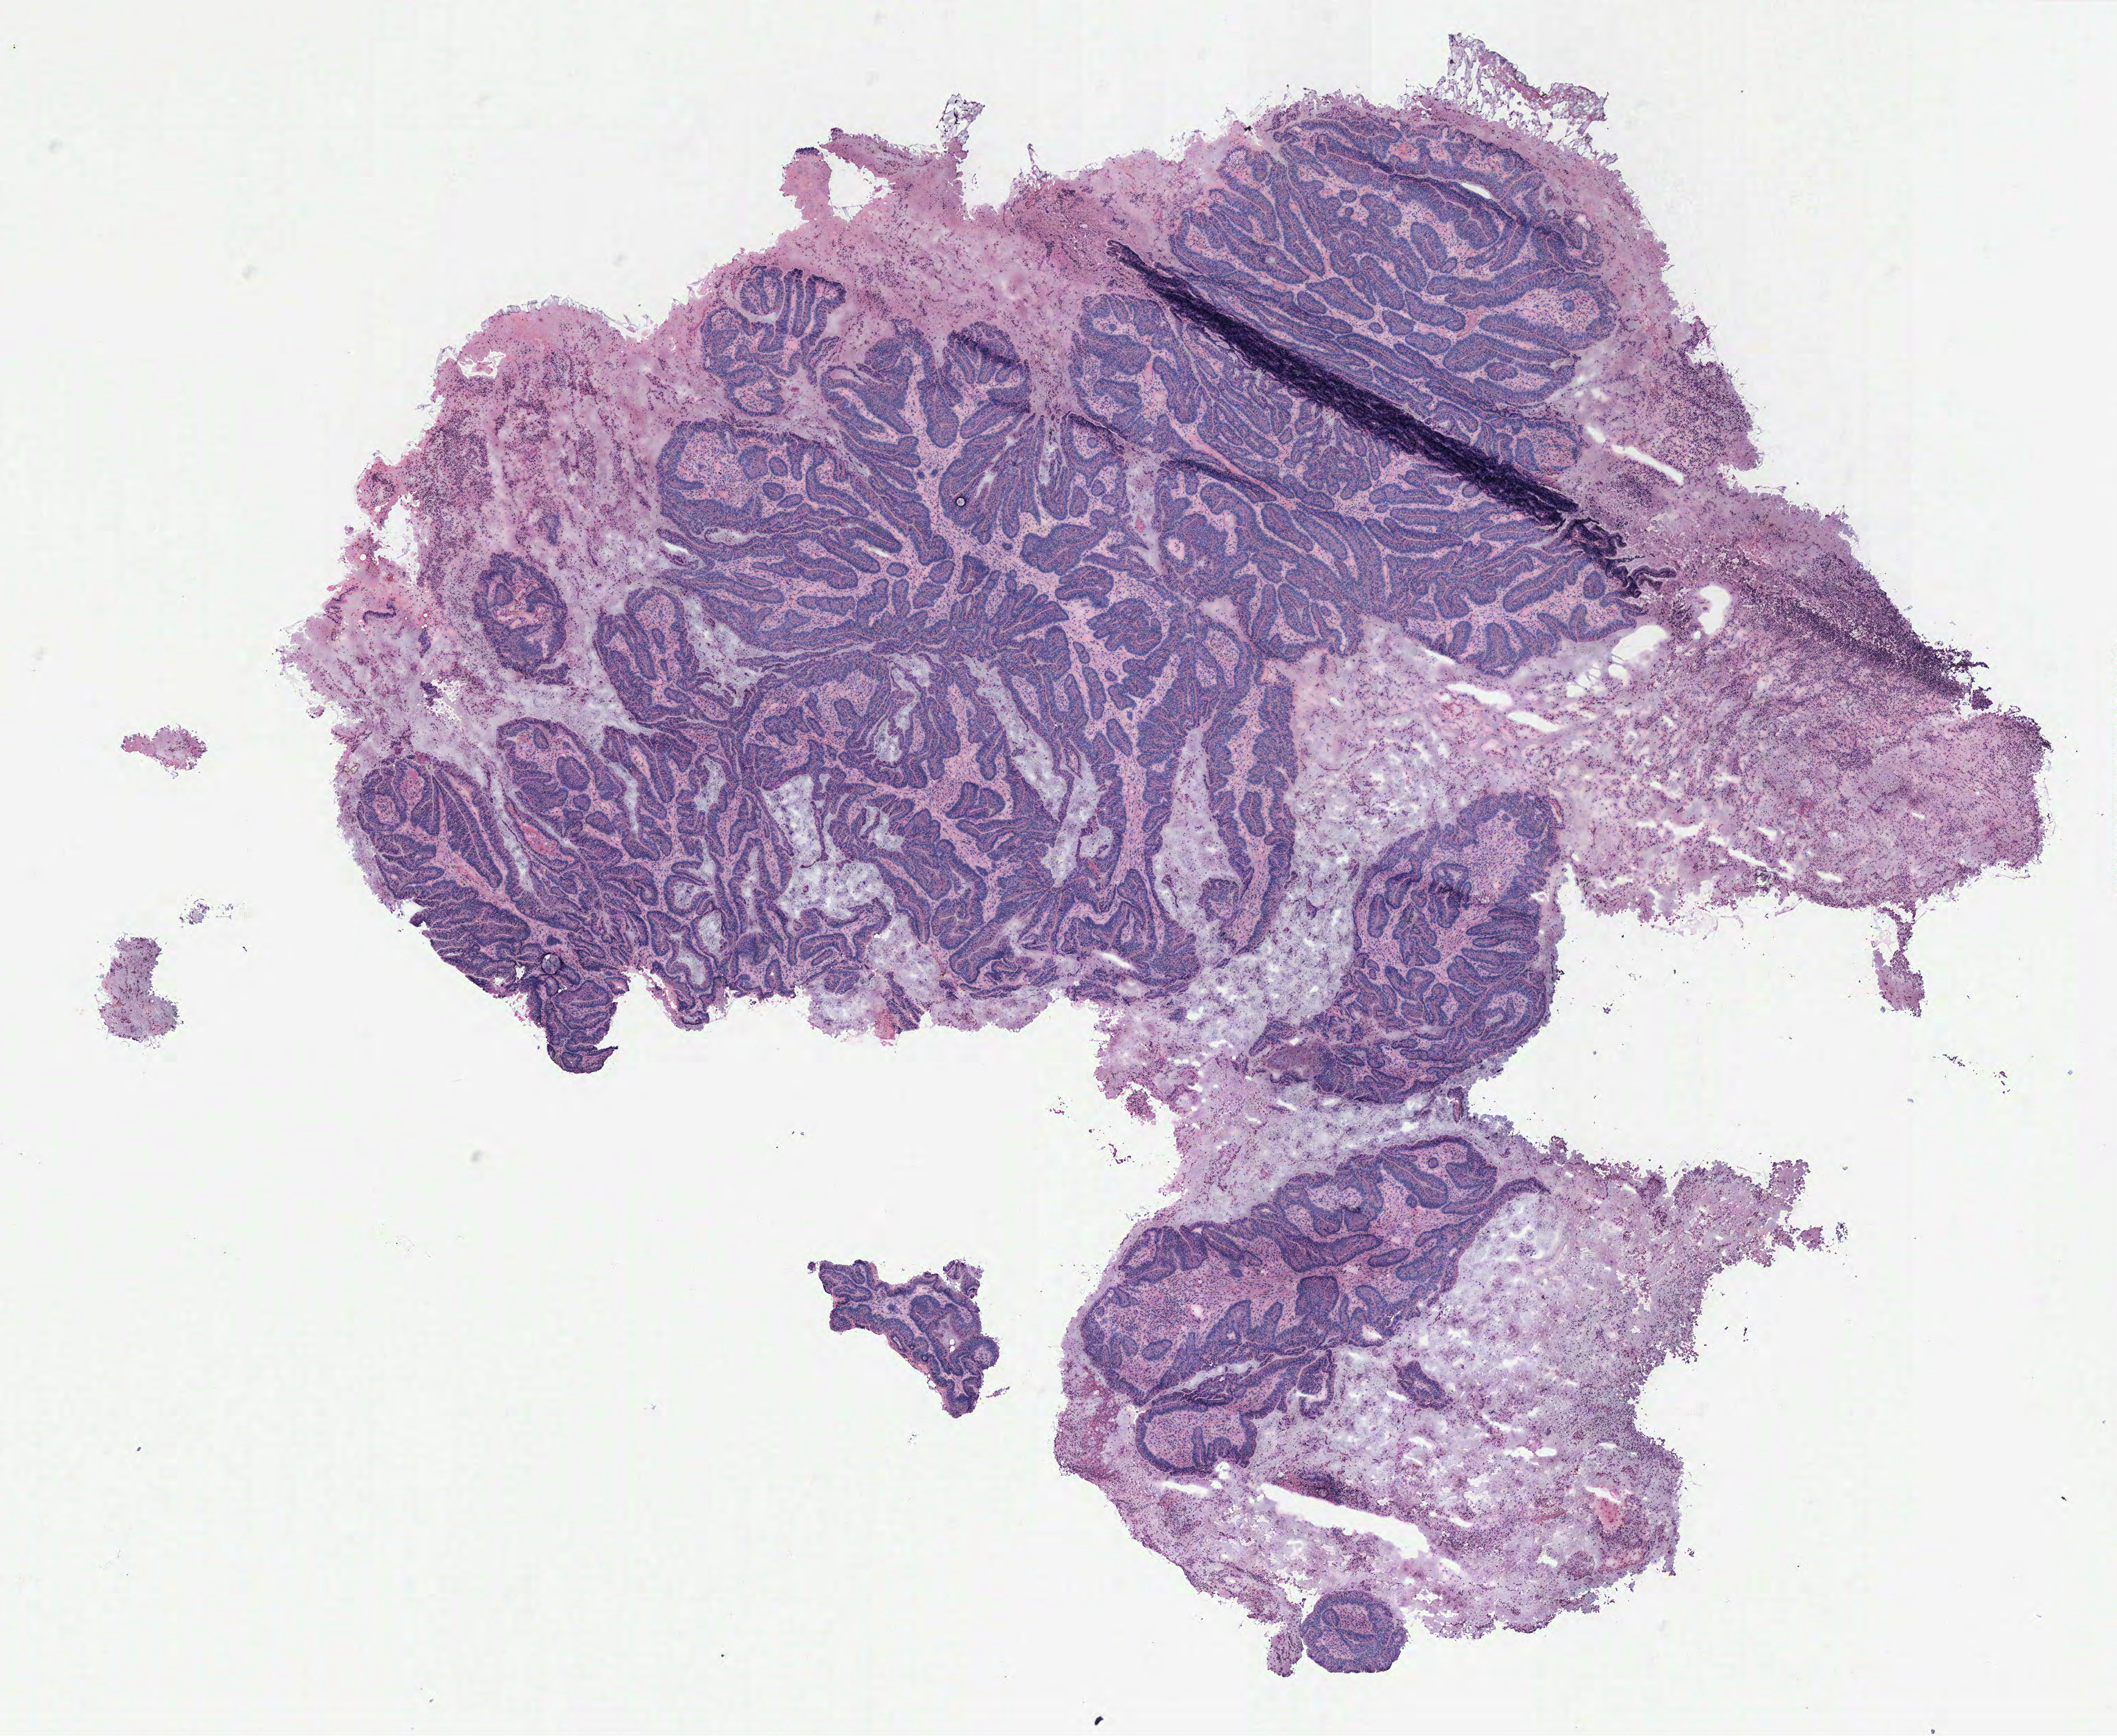
Hematoxylin and eosin (H&E) stained whole-slide image, low-resolution overview of the scanned area, about 12.2 x 10.0 mm. Normal (non-tumour) tissue sample, colon. Female, 76 y/o.
This section: normal (non-tumour) tissue from the same patient. Patient diagnosis: Adenocarcinoma, NOS.